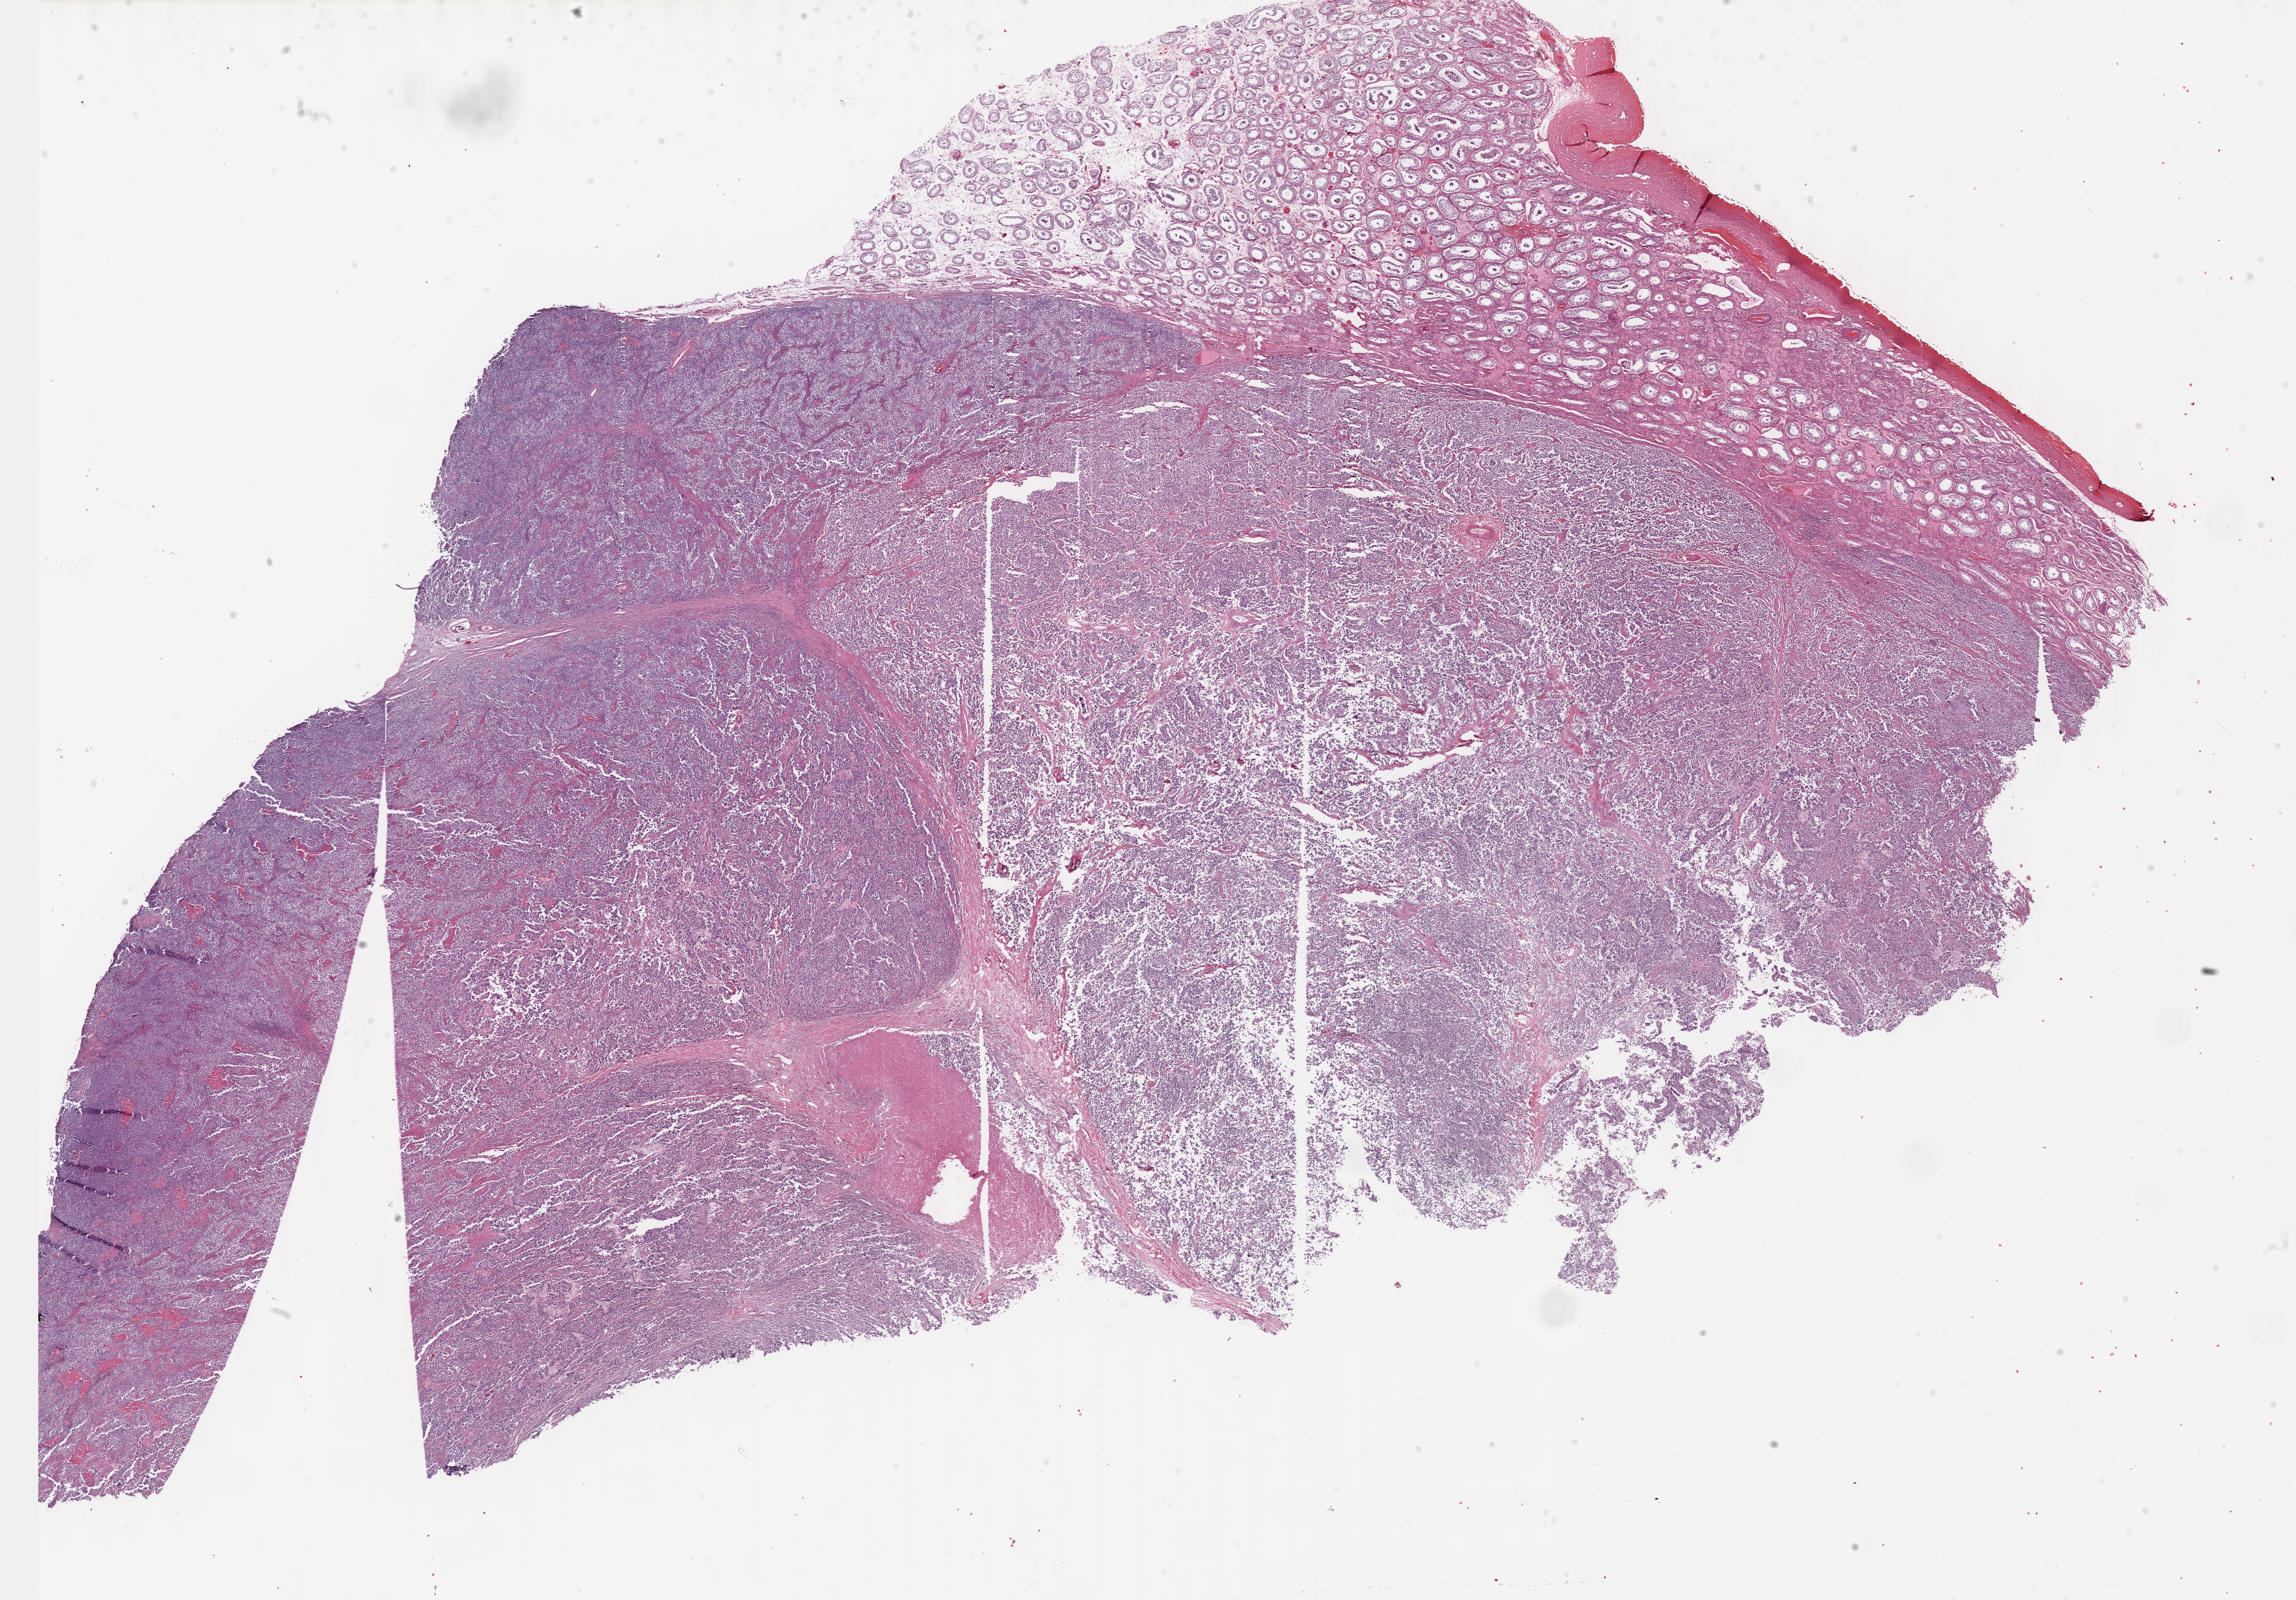
Whole-slide histology image, H&E-stained, shown as a low-resolution overview of the whole scanned area (about 30.2 x 21.0 mm, from a 40x scan). Formalin-fixed paraffin-embedded (FFPE) diagnostic section. Testis, primary tumour sample. Male patient; age at initial diagnosis 29 years.
- diagnosis: Seminoma, NOS
- AJCC pathologic stage: IS